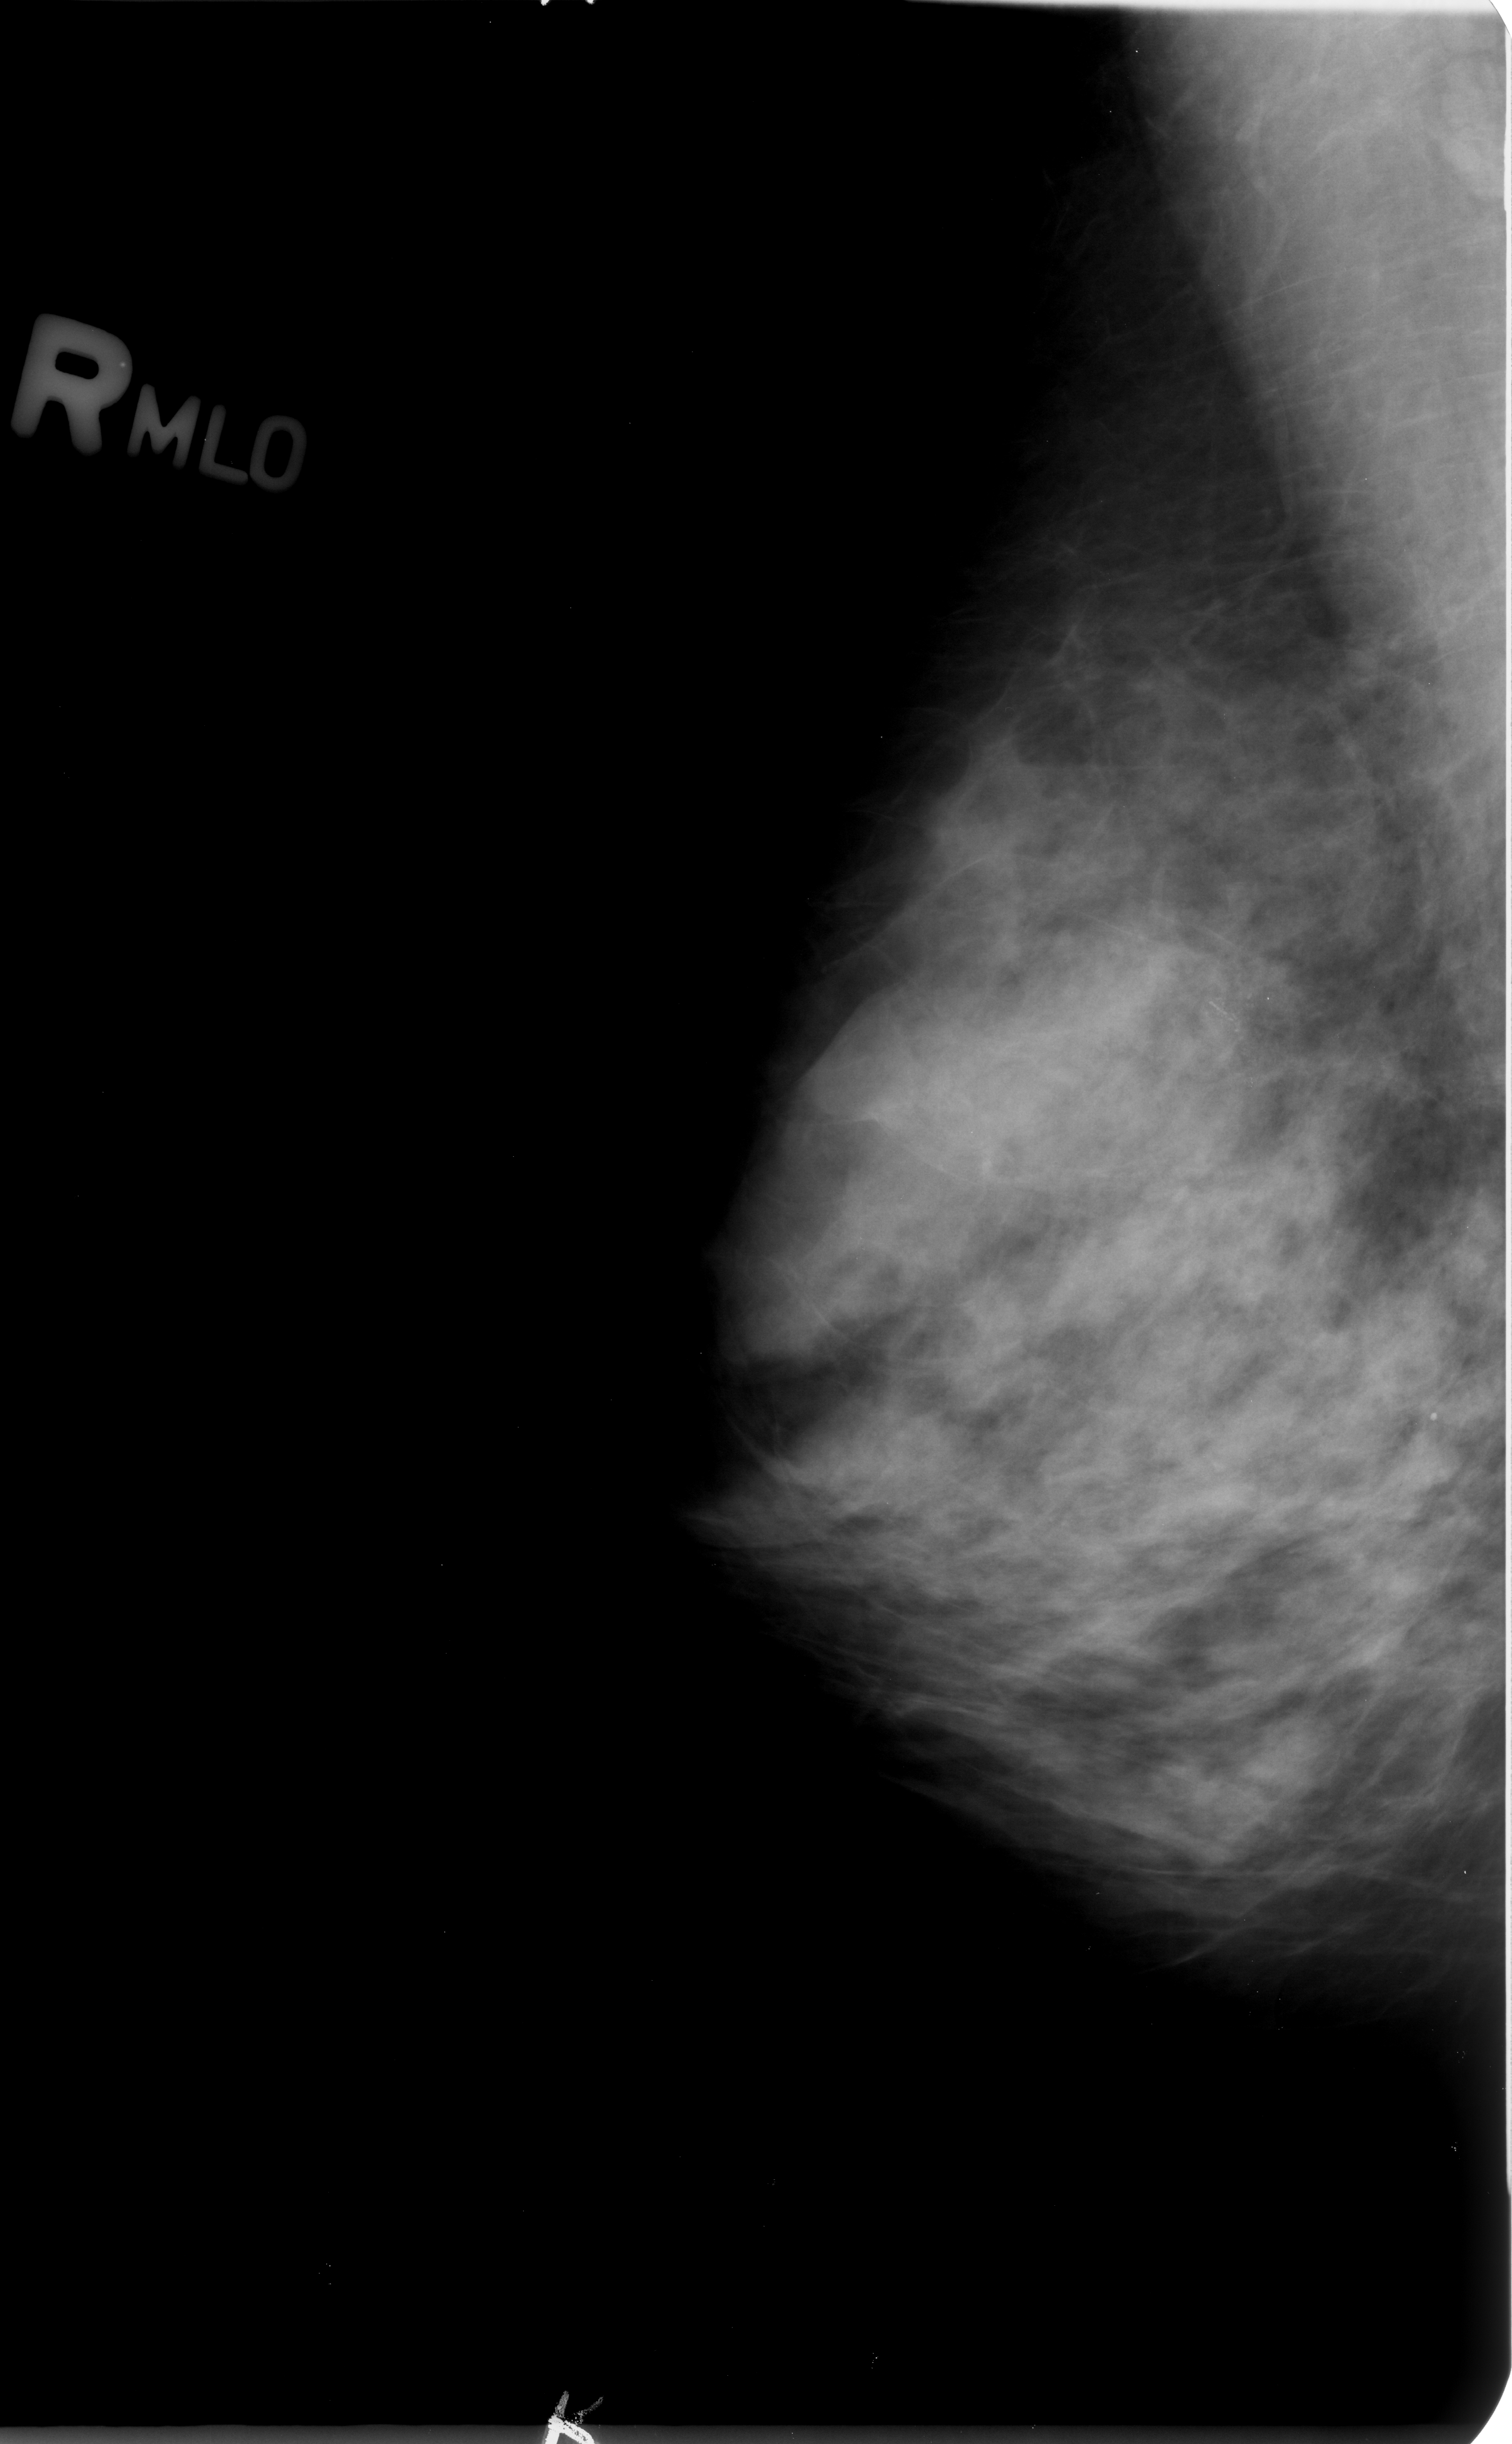
Scanned film-screen mammogram. Right breast. Mediolateral oblique (MLO) view. 1512 × 2444 image matrix.
Marked abnormalities (boxes around the expert regions of interest):
- calcifications, morphology pleomorphic, distribution clustered; BI-RADS assessment category 4; pathology (as recorded): malignant: bounding box <1152,944,1284,1073> (left, top, right, bottom; pixels)